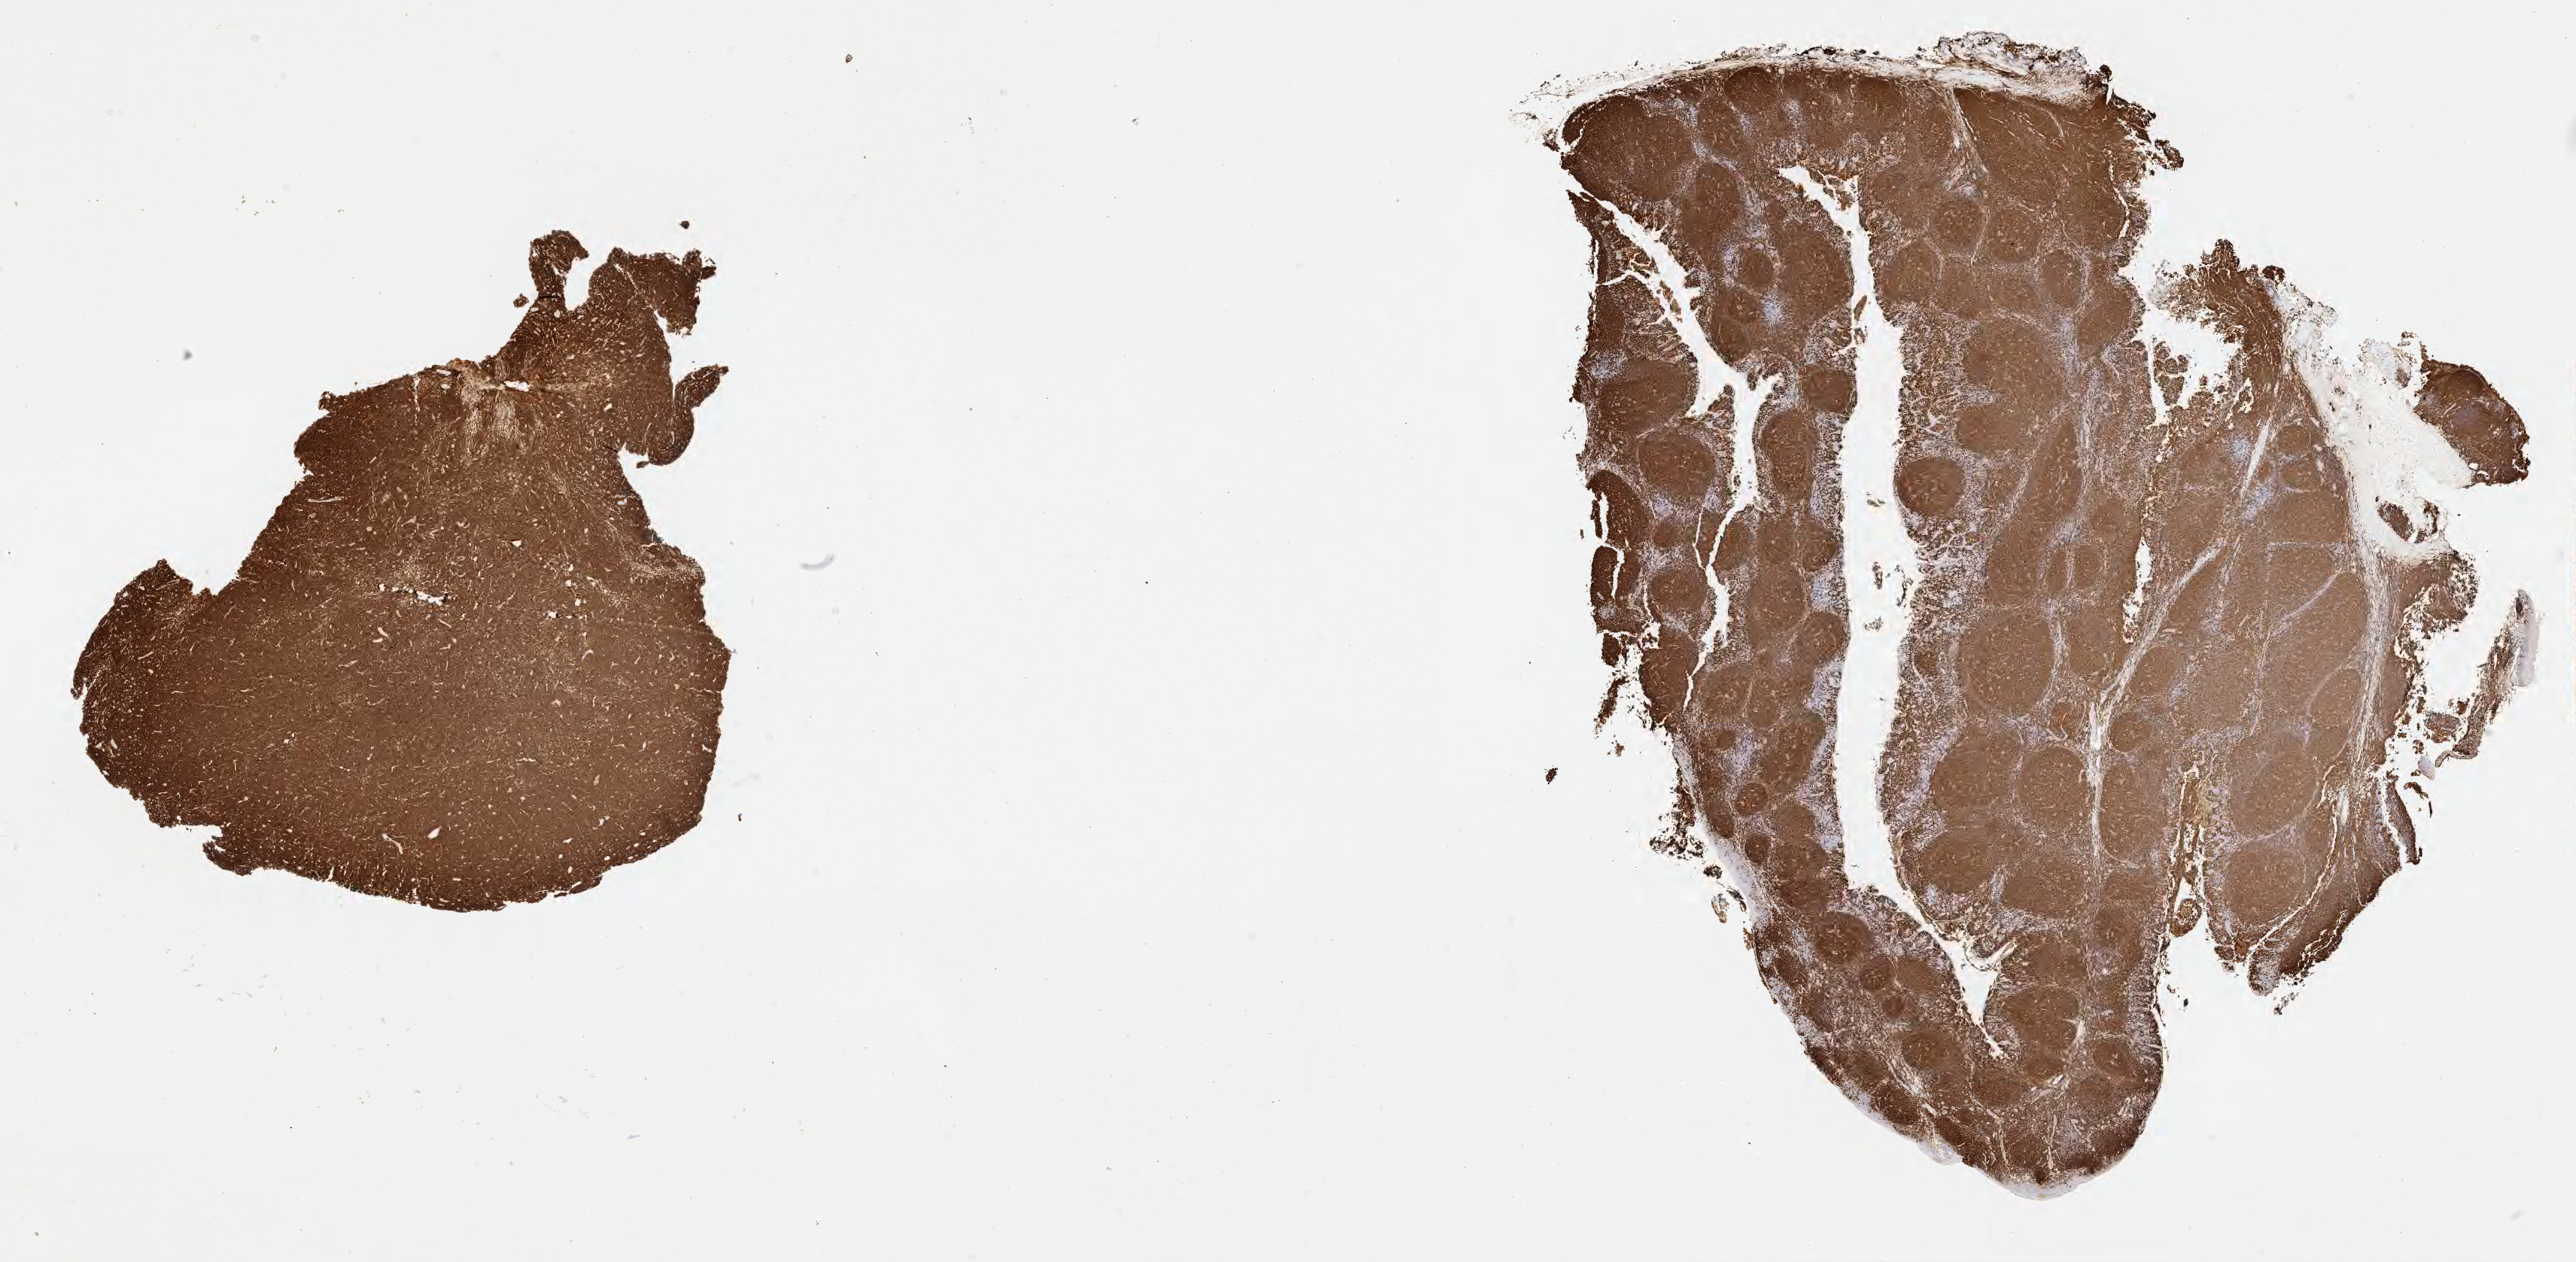
Immunohistochemistry (IHC) whole-slide image stained for CD20 — whole scanned area (about 27.7 x 13.6 mm) shown as a low-resolution overview; specimen: tumor tissue; anatomic site: mandible. Female, age 5 years at initial diagnosis.
Diagnosis: Burkitt lymphoma, NOS.